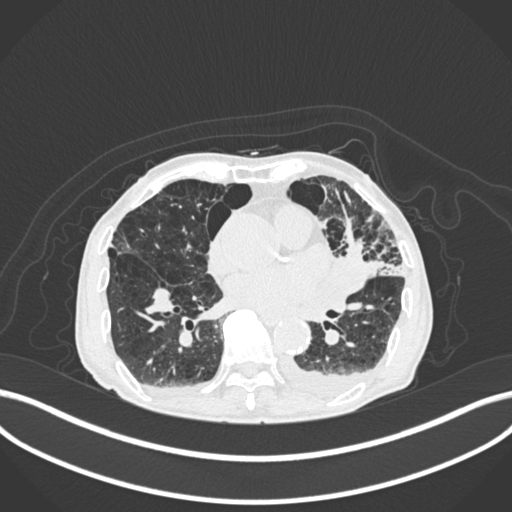
Chest CT, one axial slice. Position 89 of 400 along the scan axis. Lung window (W 1500 / L -600 HU). 512 × 512 image matrix, field of view 400 × 400 mm. Male patient, age 90 years or older. Case-level facts recorded for this patient, not image findings: clinical TNM (as recorded): T2b N1 M0.
Structures marked on this image (rectangle marked by the reading radiologist):
- lung tumour (recorded histology: squamous cell carcinoma): box from (x=337, y=239) to (x=381, y=292) px